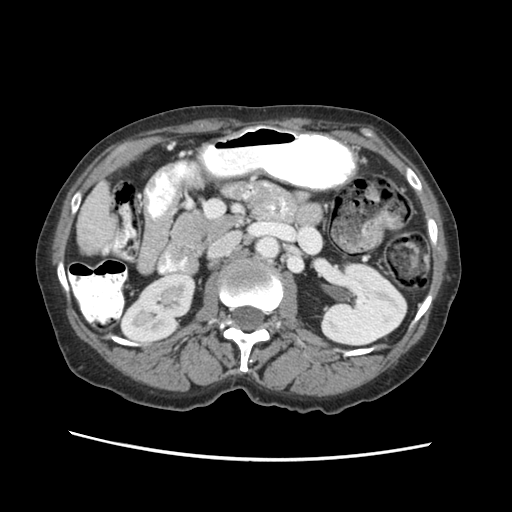
Contrast-enhanced abdominal CT (liver protocol), one axial slice. Position 10 of 63 along the scan axis. Reconstruction kernel STANDARD. 120 kVp. Soft-tissue window (W 400 / L 40 HU). 2.5 mm slice thickness. 512 × 512 image matrix, field of view 340 × 340 mm. Case-level facts recorded for this patient, not image findings: diagnosis: hepatocellular carcinoma (patient treated with transarterial chemoembolisation; whether this scan precedes or follows treatment is not stated here); TNM stage (as recorded): Stage-I; Child-Pugh class: B; tumour differentiation: well differentiated; tumour nodularity: uninodular.
Structures marked on this image (semi-automatic segmentation, software-assisted and operator-edited):
- liver parenchyma outside the tumour (the mass and vessels are separate outlines, so this box may not span the whole liver): box from (x=78, y=180) to (x=116, y=251) px